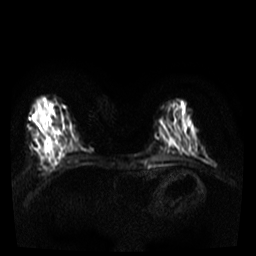
Breast MRI, one axial slice. Slice 12 of 36 in the series (ordered by position). Diffusion-weighted series; image 2 of 4 stored at this slice position (different b-values; order by instance number). 3 T. 256 × 256 image matrix, field of view 300 × 300 mm. Female patient.
Structures marked on this image (expert manual segmentation):
- tumour on diffusion-weighted imaging: bounding box (x1, y1, x2, y2) in pixels: (35, 112, 53, 153)